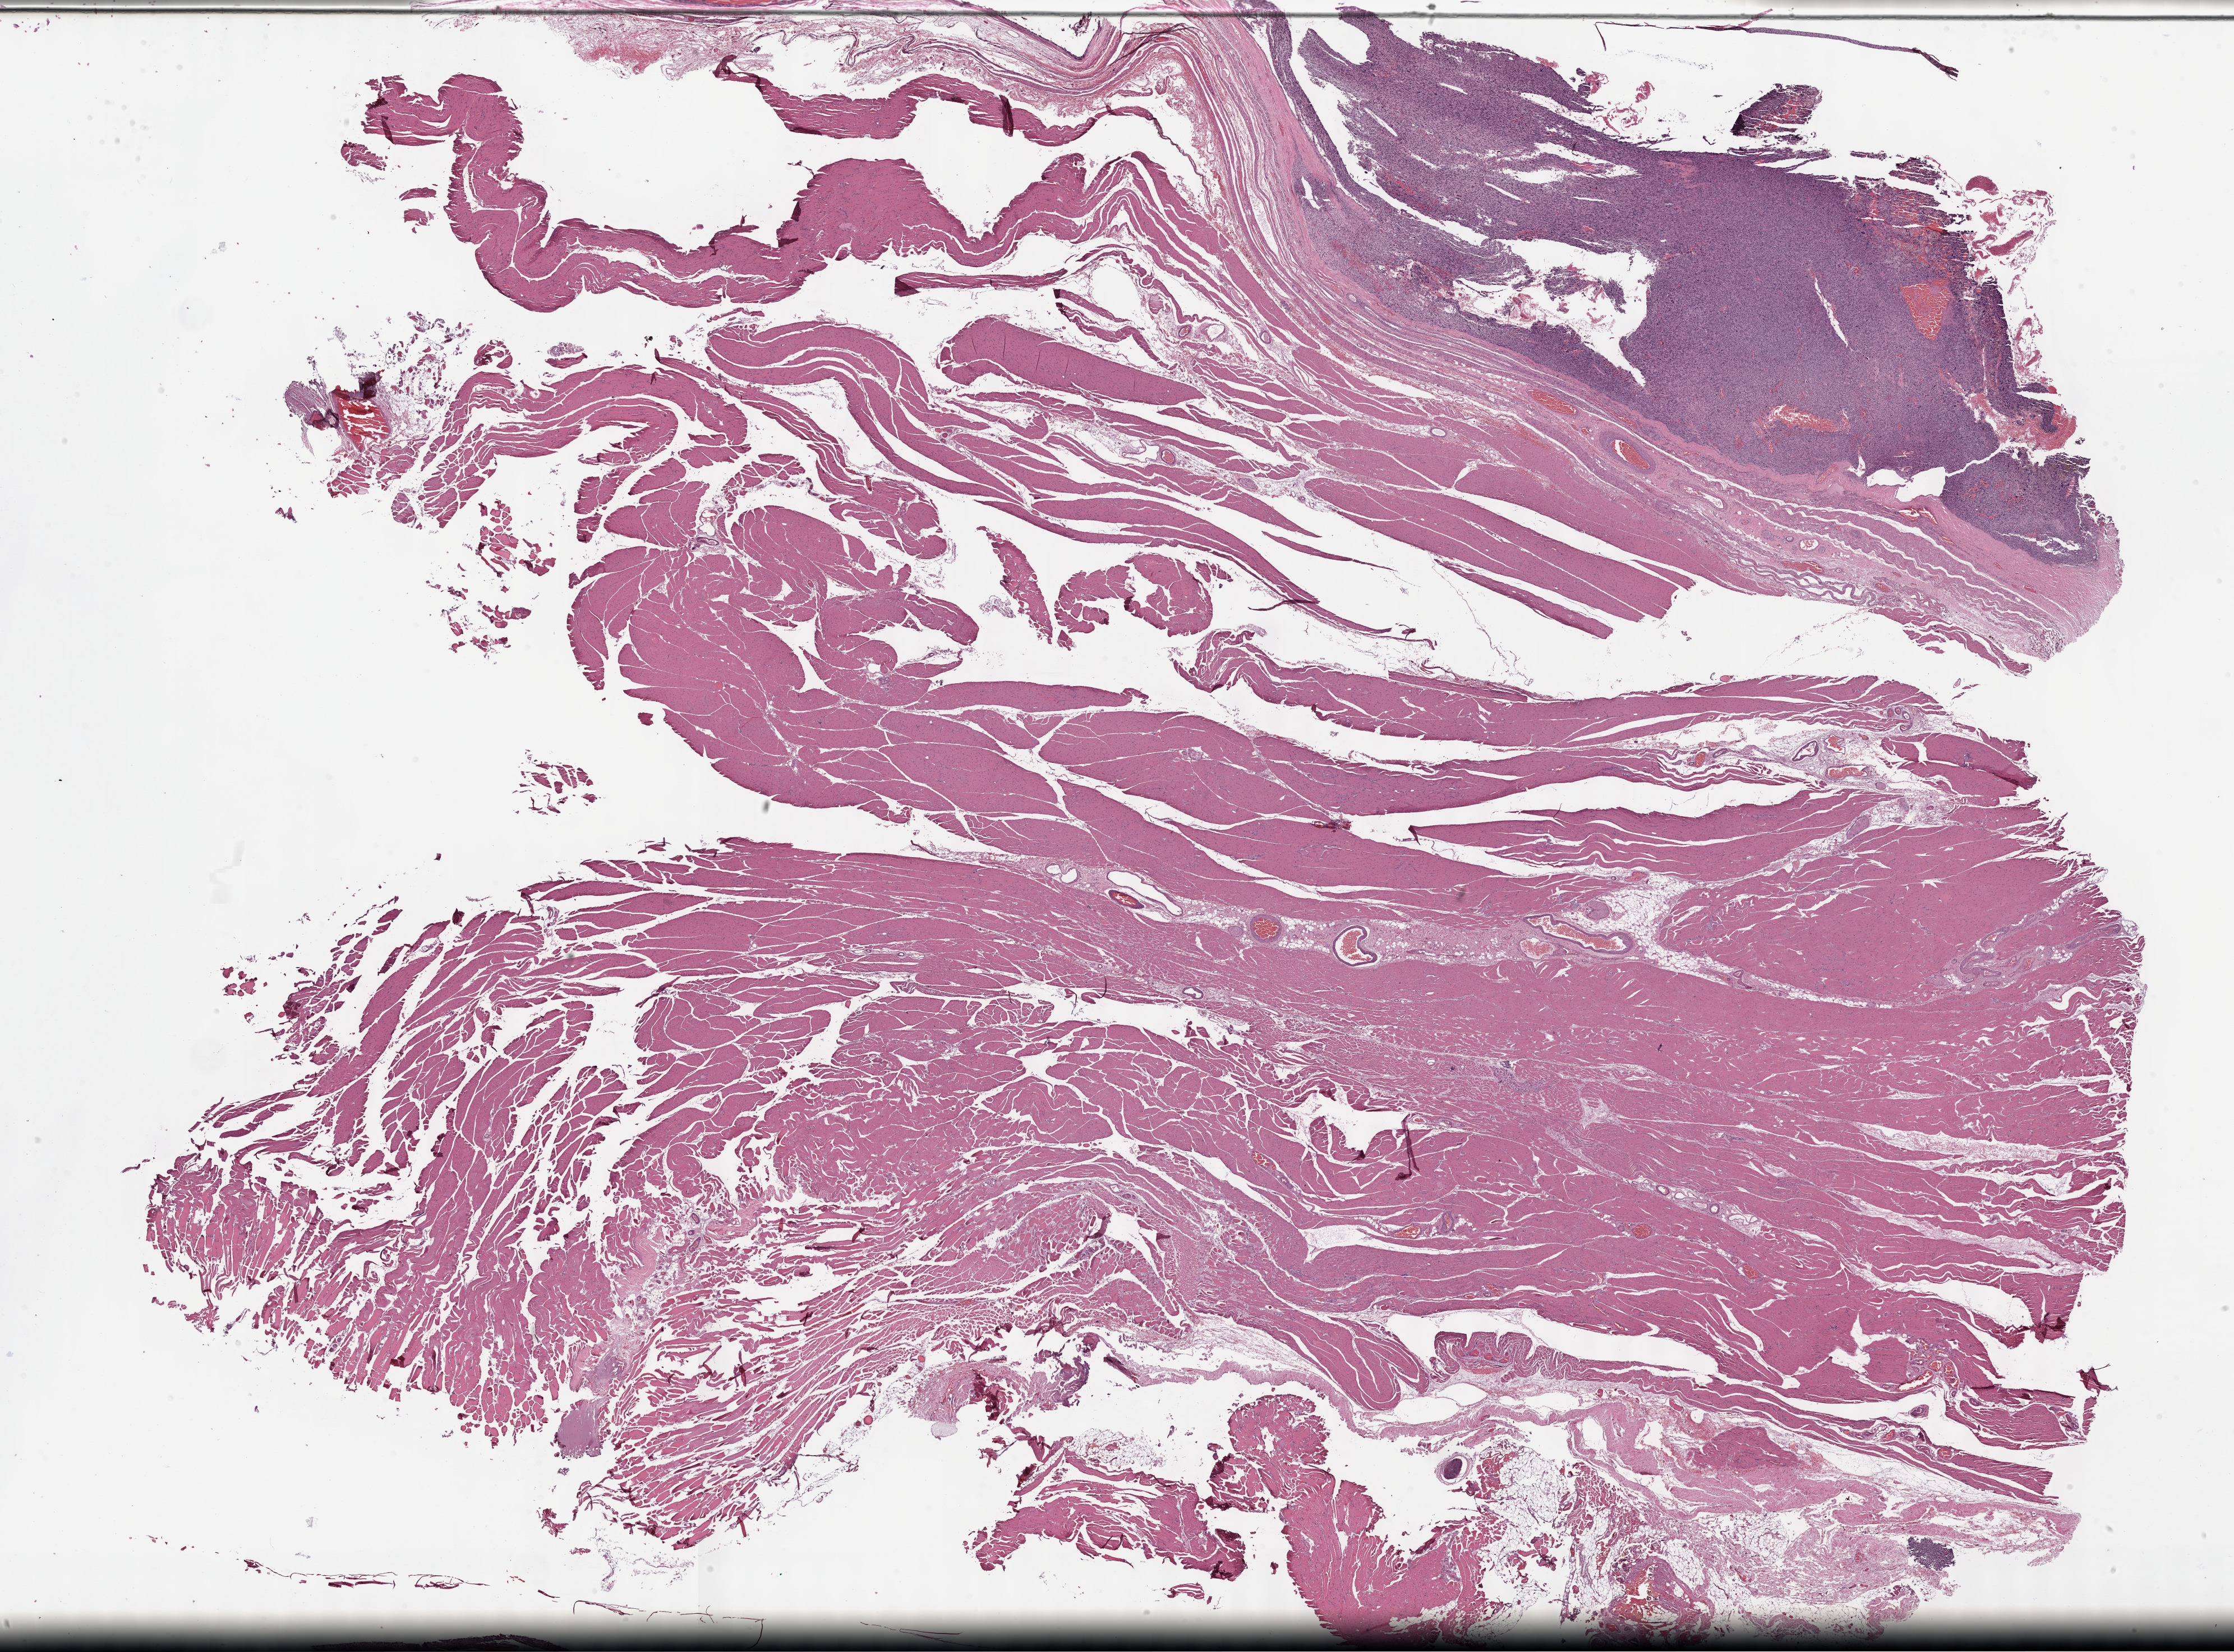
Hematoxylin and eosin (H&E) stained whole-slide image, a low-resolution overview of the entire scanned area, about 32.2 x 23.8 mm. Formalin-fixed paraffin-embedded (FFPE) diagnostic section. Primary tumour sample from the connective, subcutaneous and other soft tissues. Patient: female, age at initial diagnosis 80 years.
Diagnosis: Undifferentiated sarcoma (connective, subcutaneous and other soft tissues of lower limb and hip).